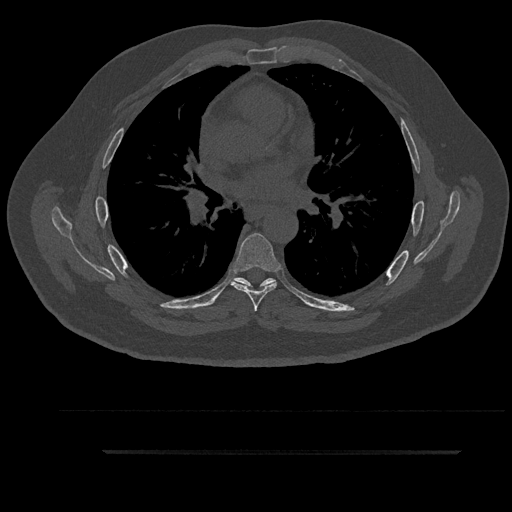
CT including the spine, one axial slice. Slice 565 of 797 in the series (ordered by position). Reconstruction kernel Br40s/3. 120 kVp. Bone window (W 1800 / L 400 HU). 512 × 512 image matrix, field of view 432 × 432 mm. Patient: male, 63 years. Case-level facts recorded for this patient, not image findings: primary cancer: renal; vertebrae with lytic lesions (as recorded): T8.
Structures marked on this image (semi-automatic segmentation, software-assisted and operator-edited):
- T5 vertebra: bounding box <235,278,266,291> (left, top, right, bottom; pixels)
- T6 vertebra: <231,233,280,312>
- T7 vertebra: <235,278,276,285>